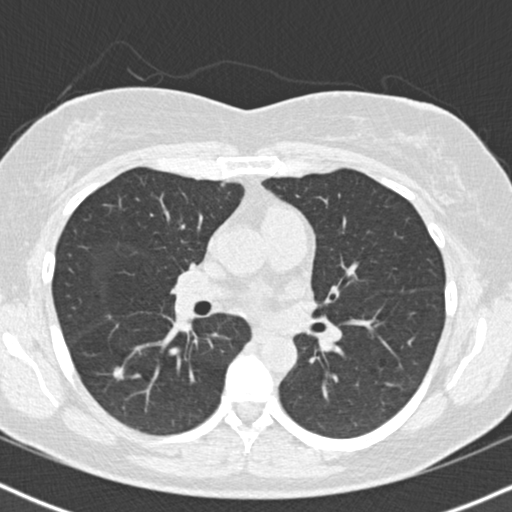
Low-dose screening chest CT, axial slice. Baseline screening round. Lung window (W 1500 / L -600 HU). 2 mm slice thickness. Slice 73 of 167 in the series. 512 × 512 image matrix. Female, age 55 years at enrolment. Former smoker at enrolment.
- Lesion marked by an expert reader, bounding box (x1, y1, x2, y2) in pixels: (86, 347, 145, 394).
- The exam's reader record, not a measurement of the box and not confirmed to be the same lesion: non-calcified nodule or mass ≥4 mm, right lower lobe, 8 × 8 mm, poorly defined margins, soft tissue attenuation.
- Official screen result: positive, change unspecified: nodule(s) >= 4 mm or enlarging nodule(s), mass(es), or other non-specific abnormalities suspicious for lung cancer.
- Lung cancer was diagnosed 14 days after this screen: bronchiolo-alveolar adenocarcinoma, NOS, right lower lobe, well differentiated (G1), stage IA (AJCC 6th edition), 12 mm at pathology.